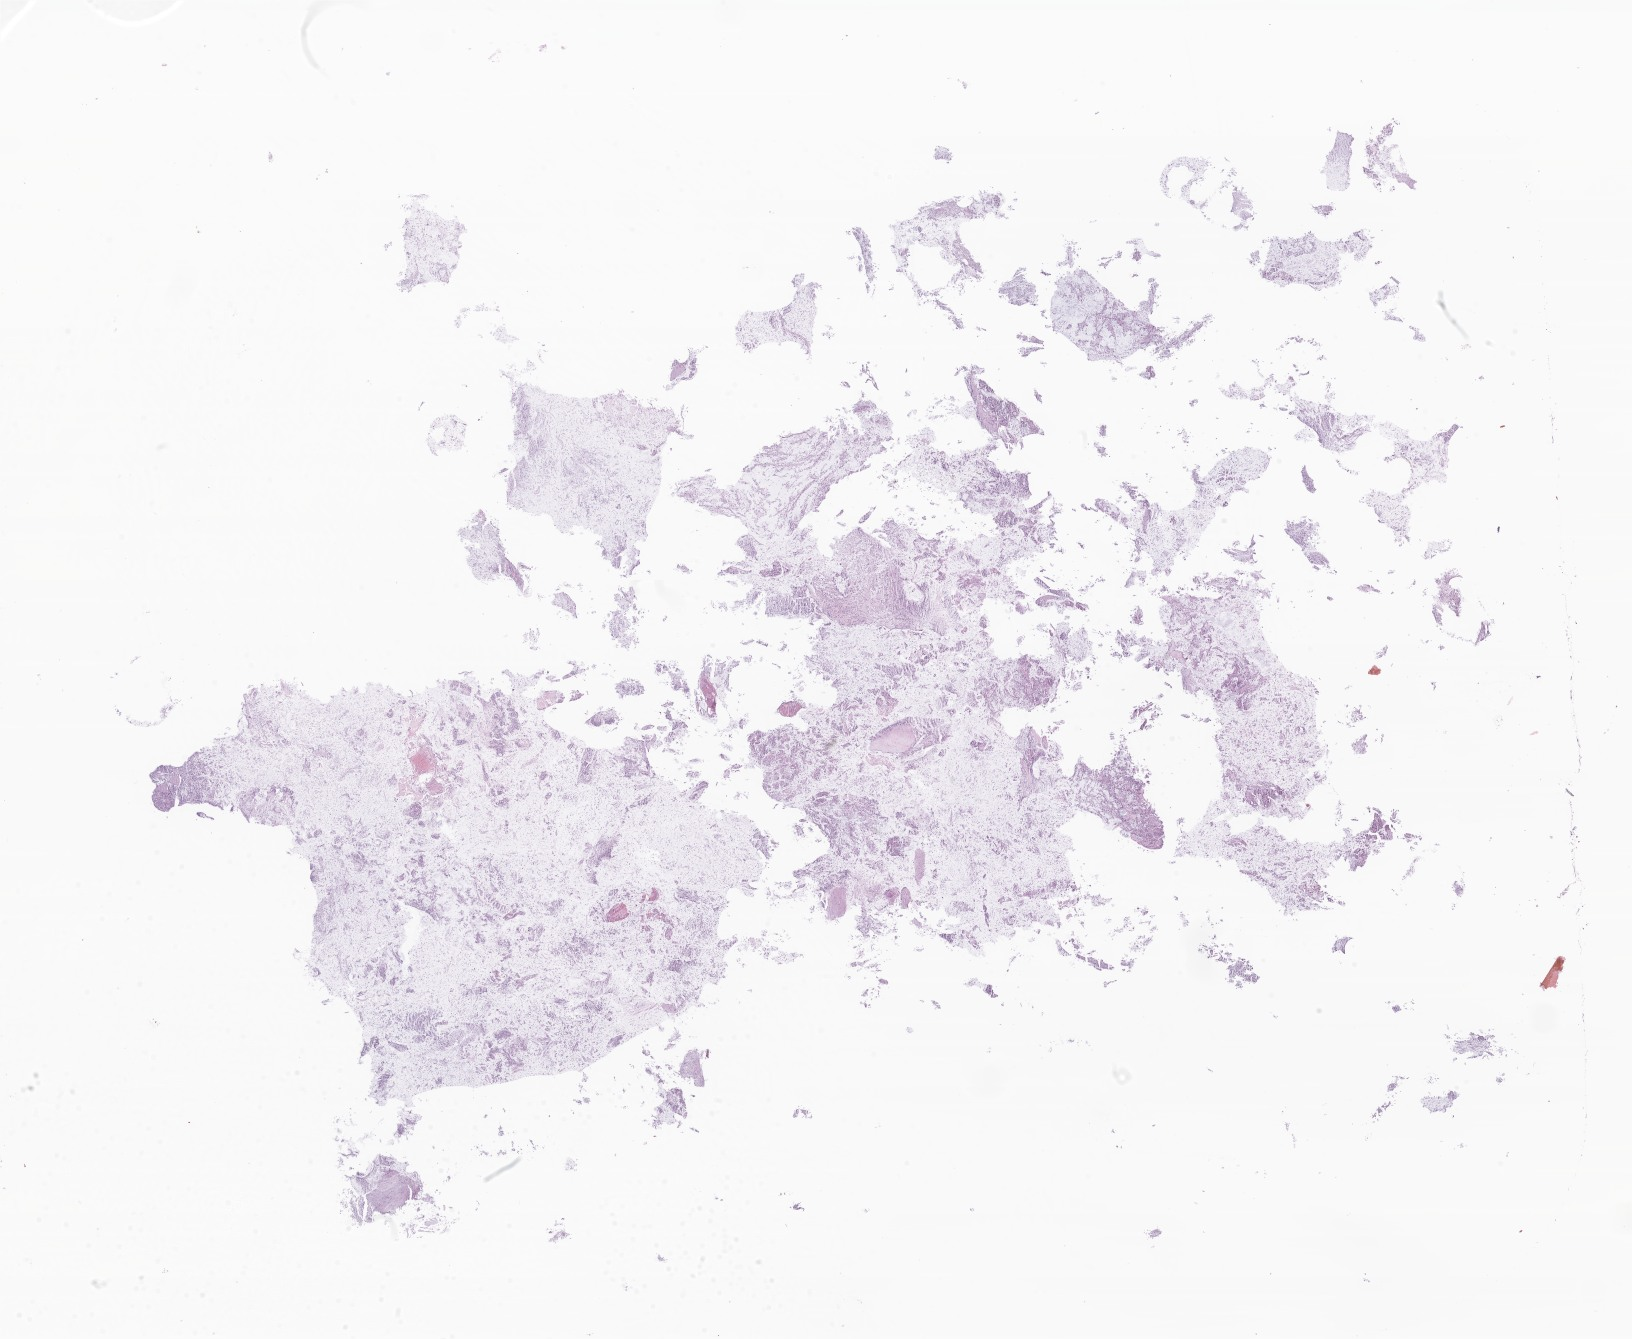
Digitized H&E-stained section of tumor tissue from the brain — shown as a low-resolution overview of the whole scanned area (about 27.5 x 22.6 mm), formalin-fixed paraffin-embedded section. Male patient, age 219 months (18 years 3 months).
• diagnosis: Pilocytic astrocytoma